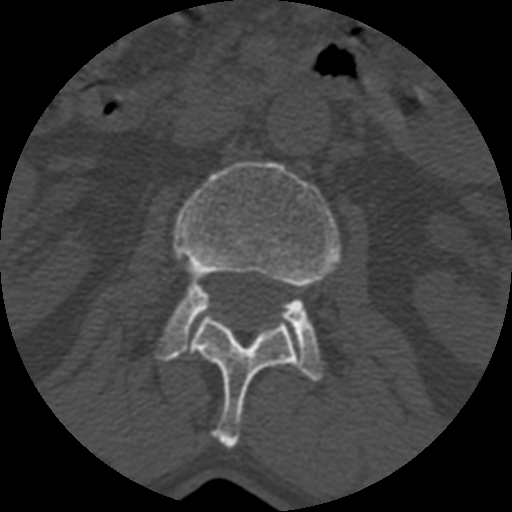
CT including the spine, one axial slice. Position 346 of 399 along the scan axis. Reconstruction kernel STANDARD. 120 kVp. Bone window (W 1800 / L 400 HU). 512 × 512 image matrix, field of view 160 × 160 mm. Patient age 71 years. Case-level facts recorded for this patient, not image findings: primary cancer: prostate.
Structures marked on this image (semi-automatic segmentation, software-assisted and operator-edited):
- L1 vertebra: box from (x=186, y=314) to (x=297, y=447) px
- L2 vertebra: (x=157, y=160)–(x=340, y=381)